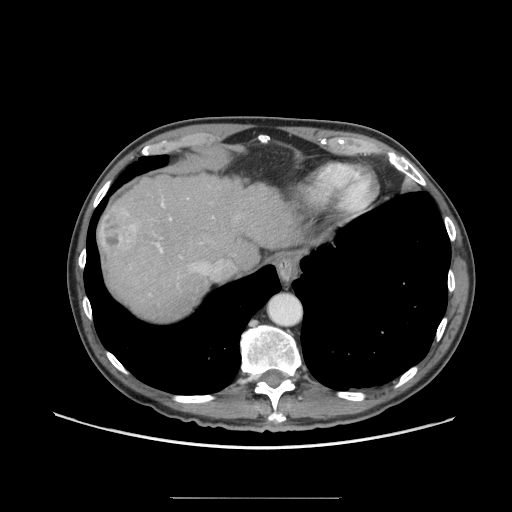
Contrast-enhanced abdominal CT (liver protocol), one axial slice; slice 56 of 71 in the series (ordered by position); reconstruction kernel STANDARD; 140 kVp; soft-tissue window (W 400 / L 40 HU); 2.5 mm slice thickness; 512 × 512 image matrix. From the clinical record (not read from this slice): diagnosis: hepatocellular carcinoma (patient treated with transarterial chemoembolisation; whether this scan precedes or follows treatment is not stated here); TNM stage (as recorded): Stage-I; Child-Pugh class: A; tumour differentiation: well differentiated.
Outlined on this slice (semi-automatic segmentation, software-assisted and operator-edited):
- abdominal aorta: bounding box (x1, y1, x2, y2) in pixels: (269, 295, 301, 325)
- liver parenchyma outside the tumour (the mass and vessels are separate outlines, so this box may not span the whole liver): (98, 174, 302, 320)
- mass: (98, 203, 139, 256)
- liver vessels: (156, 201, 221, 275)